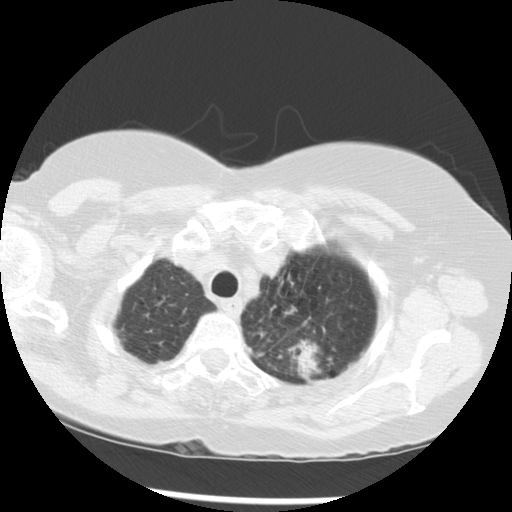
Low-dose screening chest CT, axial slice; third annual screen; lung window (W 1500 / L -600 HU); standard (soft-tissue) reconstruction kernel (STANDARD); slice 244 of 283 in the series. Female, age 70 years at enrolment. Current smoker at enrolment.
Expert-annotated lung lesion, bounding box <246,293,345,381> (left, top, right, bottom; pixels). The exam's reader record, not a measurement of the box and not confirmed to be the same lesion: non-calcified nodule or mass ≥4 mm, left upper lobe, 32 × 26 mm, spiculated (stellate) margins, soft tissue attenuation, pre-existing on the prior screen: yes; interval growth: yes. Official screen result: positive, other.